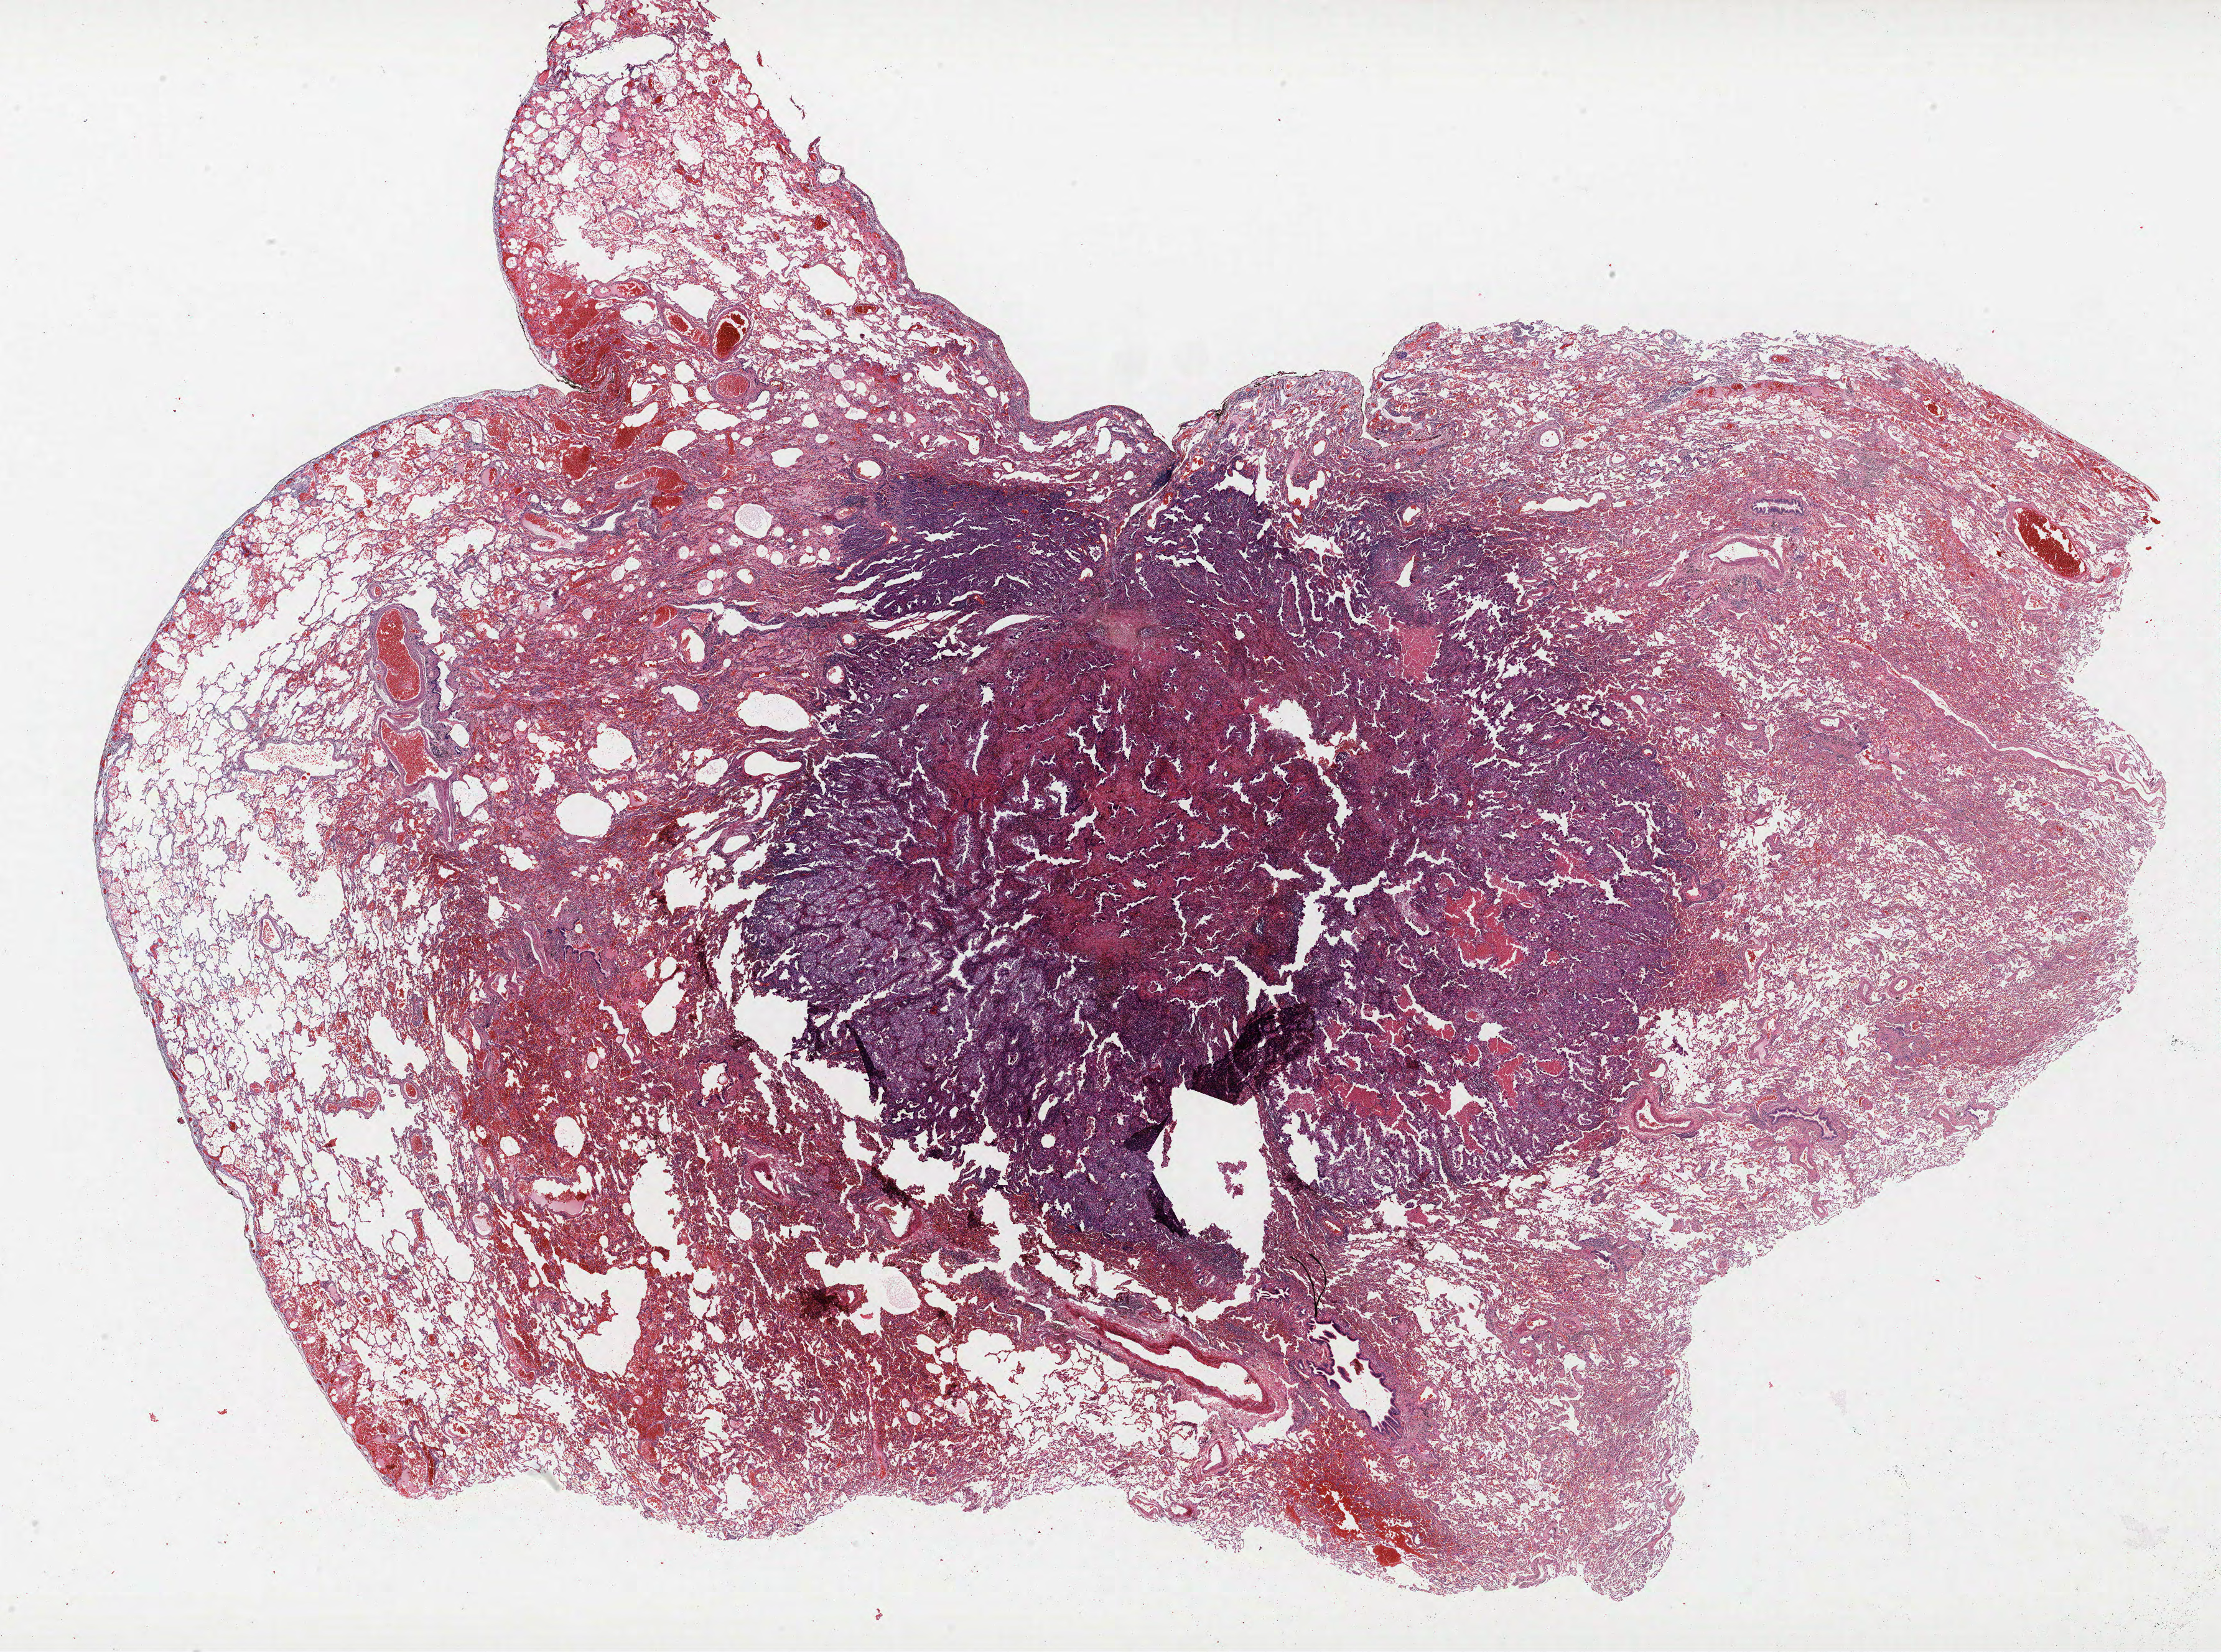
Whole-slide histology image, H&E, low-resolution overview of the scanned area, about 28.6 x 21.3 mm (acquisition: 40x scan), FFPE section, lung tissue. Female patient, aged 59 at enrolment. Current smoker at enrolment. Grade: moderately differentiated (G2).
• tumour size (pathology): 12 mm
• participant's lung-cancer diagnosis: Adenocarcinoma, NOS
• stage (AJCC 6th edition): IIIA
• primary tumour location (clinical record): right lower lobe
• ICD-O-3 topography: lower lobe of lung (C34.3)